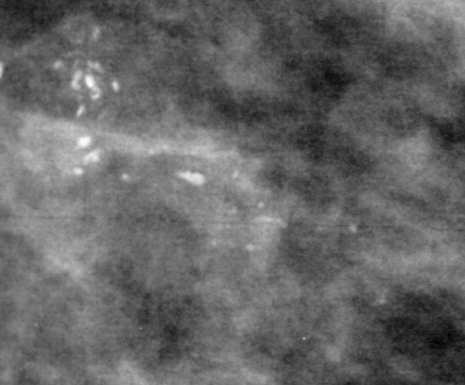
Crop from a digitized film mammogram around one marked abnormality; right breast; MLO view; BI-RADS breast density category 3 (scale 1–4).
Marked abnormality: calcifications, morphology pleomorphic, distribution clustered; BI-RADS assessment category 4; pathology (as recorded): malignant.